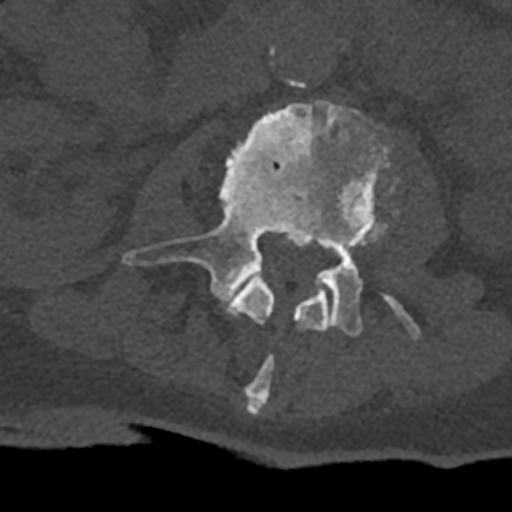
CT including the spine, one axial slice. Slice 340 of 797 in the series (ordered by position). 120 kVp. Bone window (W 1800 / L 400 HU). 512 × 512 image matrix, field of view 160 × 160 mm. Male patient, age 74 years. From the clinical record (not read from this slice): primary cancer: renal.
Outlined on this slice (semi-automatically segmented with operator editing):
- L2 vertebra: box from (x=228, y=269) to (x=330, y=415) px
- L3 vertebra: (x=122, y=100)–(x=419, y=339)